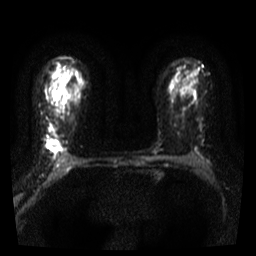
Breast MRI, one axial slice; slice 26 of 36 in the series (ordered by position); diffusion-weighted series; image 2 of 4 stored at this slice position (different b-values; order by instance number); 3 T; 5 mm slice thickness; 256 × 256 image matrix. Female patient.
Structures marked on this image (manually delineated by an expert):
- tumour on diffusion-weighted imaging: box from (x=48, y=130) to (x=61, y=152) px